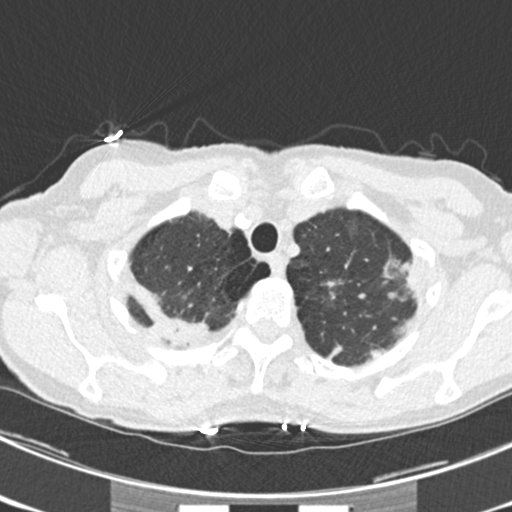
Axial slice from a low-dose chest CT screening exam; third screening round (two years after baseline); lung window (W 1500 / L -600 HU); 512 × 512 image matrix. Female participant, aged 63 years at enrolment.
- Expert-annotated lung lesion, box from (x=371, y=245) to (x=435, y=309) px.
- The screening reader recorded 9 non-calcified nodules or masses ≥4 mm on this exam; which of them this box marks is not recorded.
- Official screen result: positive, other.
- Later outcome: lung cancer diagnosed 15 days after this screen — bronchiolo-alveolar adenocarcinoma, NOS, right upper lobe, right middle lobe, right lower lobe, left upper lobe, left lower lobe, moderately differentiated (G2), stage IV (AJCC 6th edition).